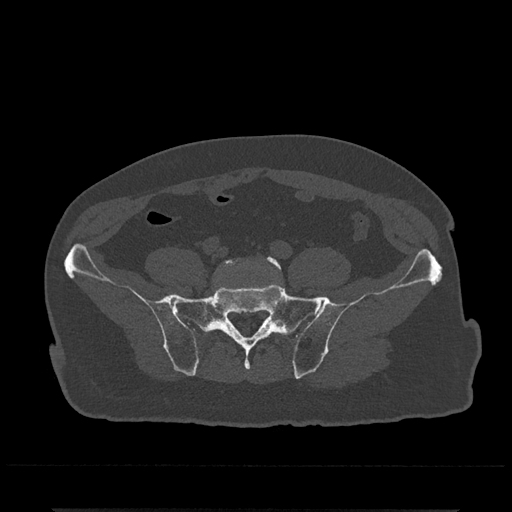
CT including the spine, one axial slice; slice 36 of 797 in the series (ordered by position); 120 kVp; bone window (W 1800 / L 400 HU); 0.5 mm slice thickness; 512 × 512 image matrix, field of view 393 × 393 mm. Male patient, age 67 years. Case-level facts recorded for this patient, not image findings: primary cancer: prostate.
Outlined on this slice (semi-automatic segmentation, software-assisted and operator-edited):
- L5 vertebra: box from (x=220, y=256) to (x=284, y=291) px